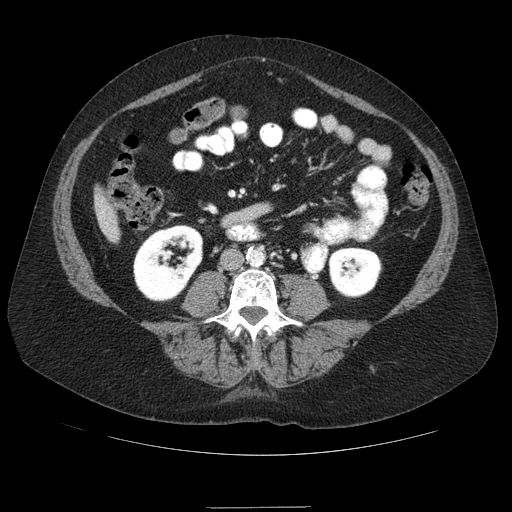
Contrast-enhanced abdominal CT (liver protocol), one axial slice; slice 11 of 89 in the series (ordered by position); soft-tissue window (W 400 / L 40 HU); 512 × 512 image matrix, field of view 400 × 400 mm. From the clinical record (not read from this slice): diagnosis: hepatocellular carcinoma (patient treated with transarterial chemoembolisation; whether this scan precedes or follows treatment is not stated here); TNM stage (as recorded): Stage-IIIB; Child-Pugh class: A.
Annotated regions visible in this slice (semi-automatic segmentation, software-assisted and operator-edited):
- liver parenchyma outside the tumour (the mass and vessels are separate outlines, so this box may not span the whole liver): box from (x=94, y=190) to (x=120, y=242) px